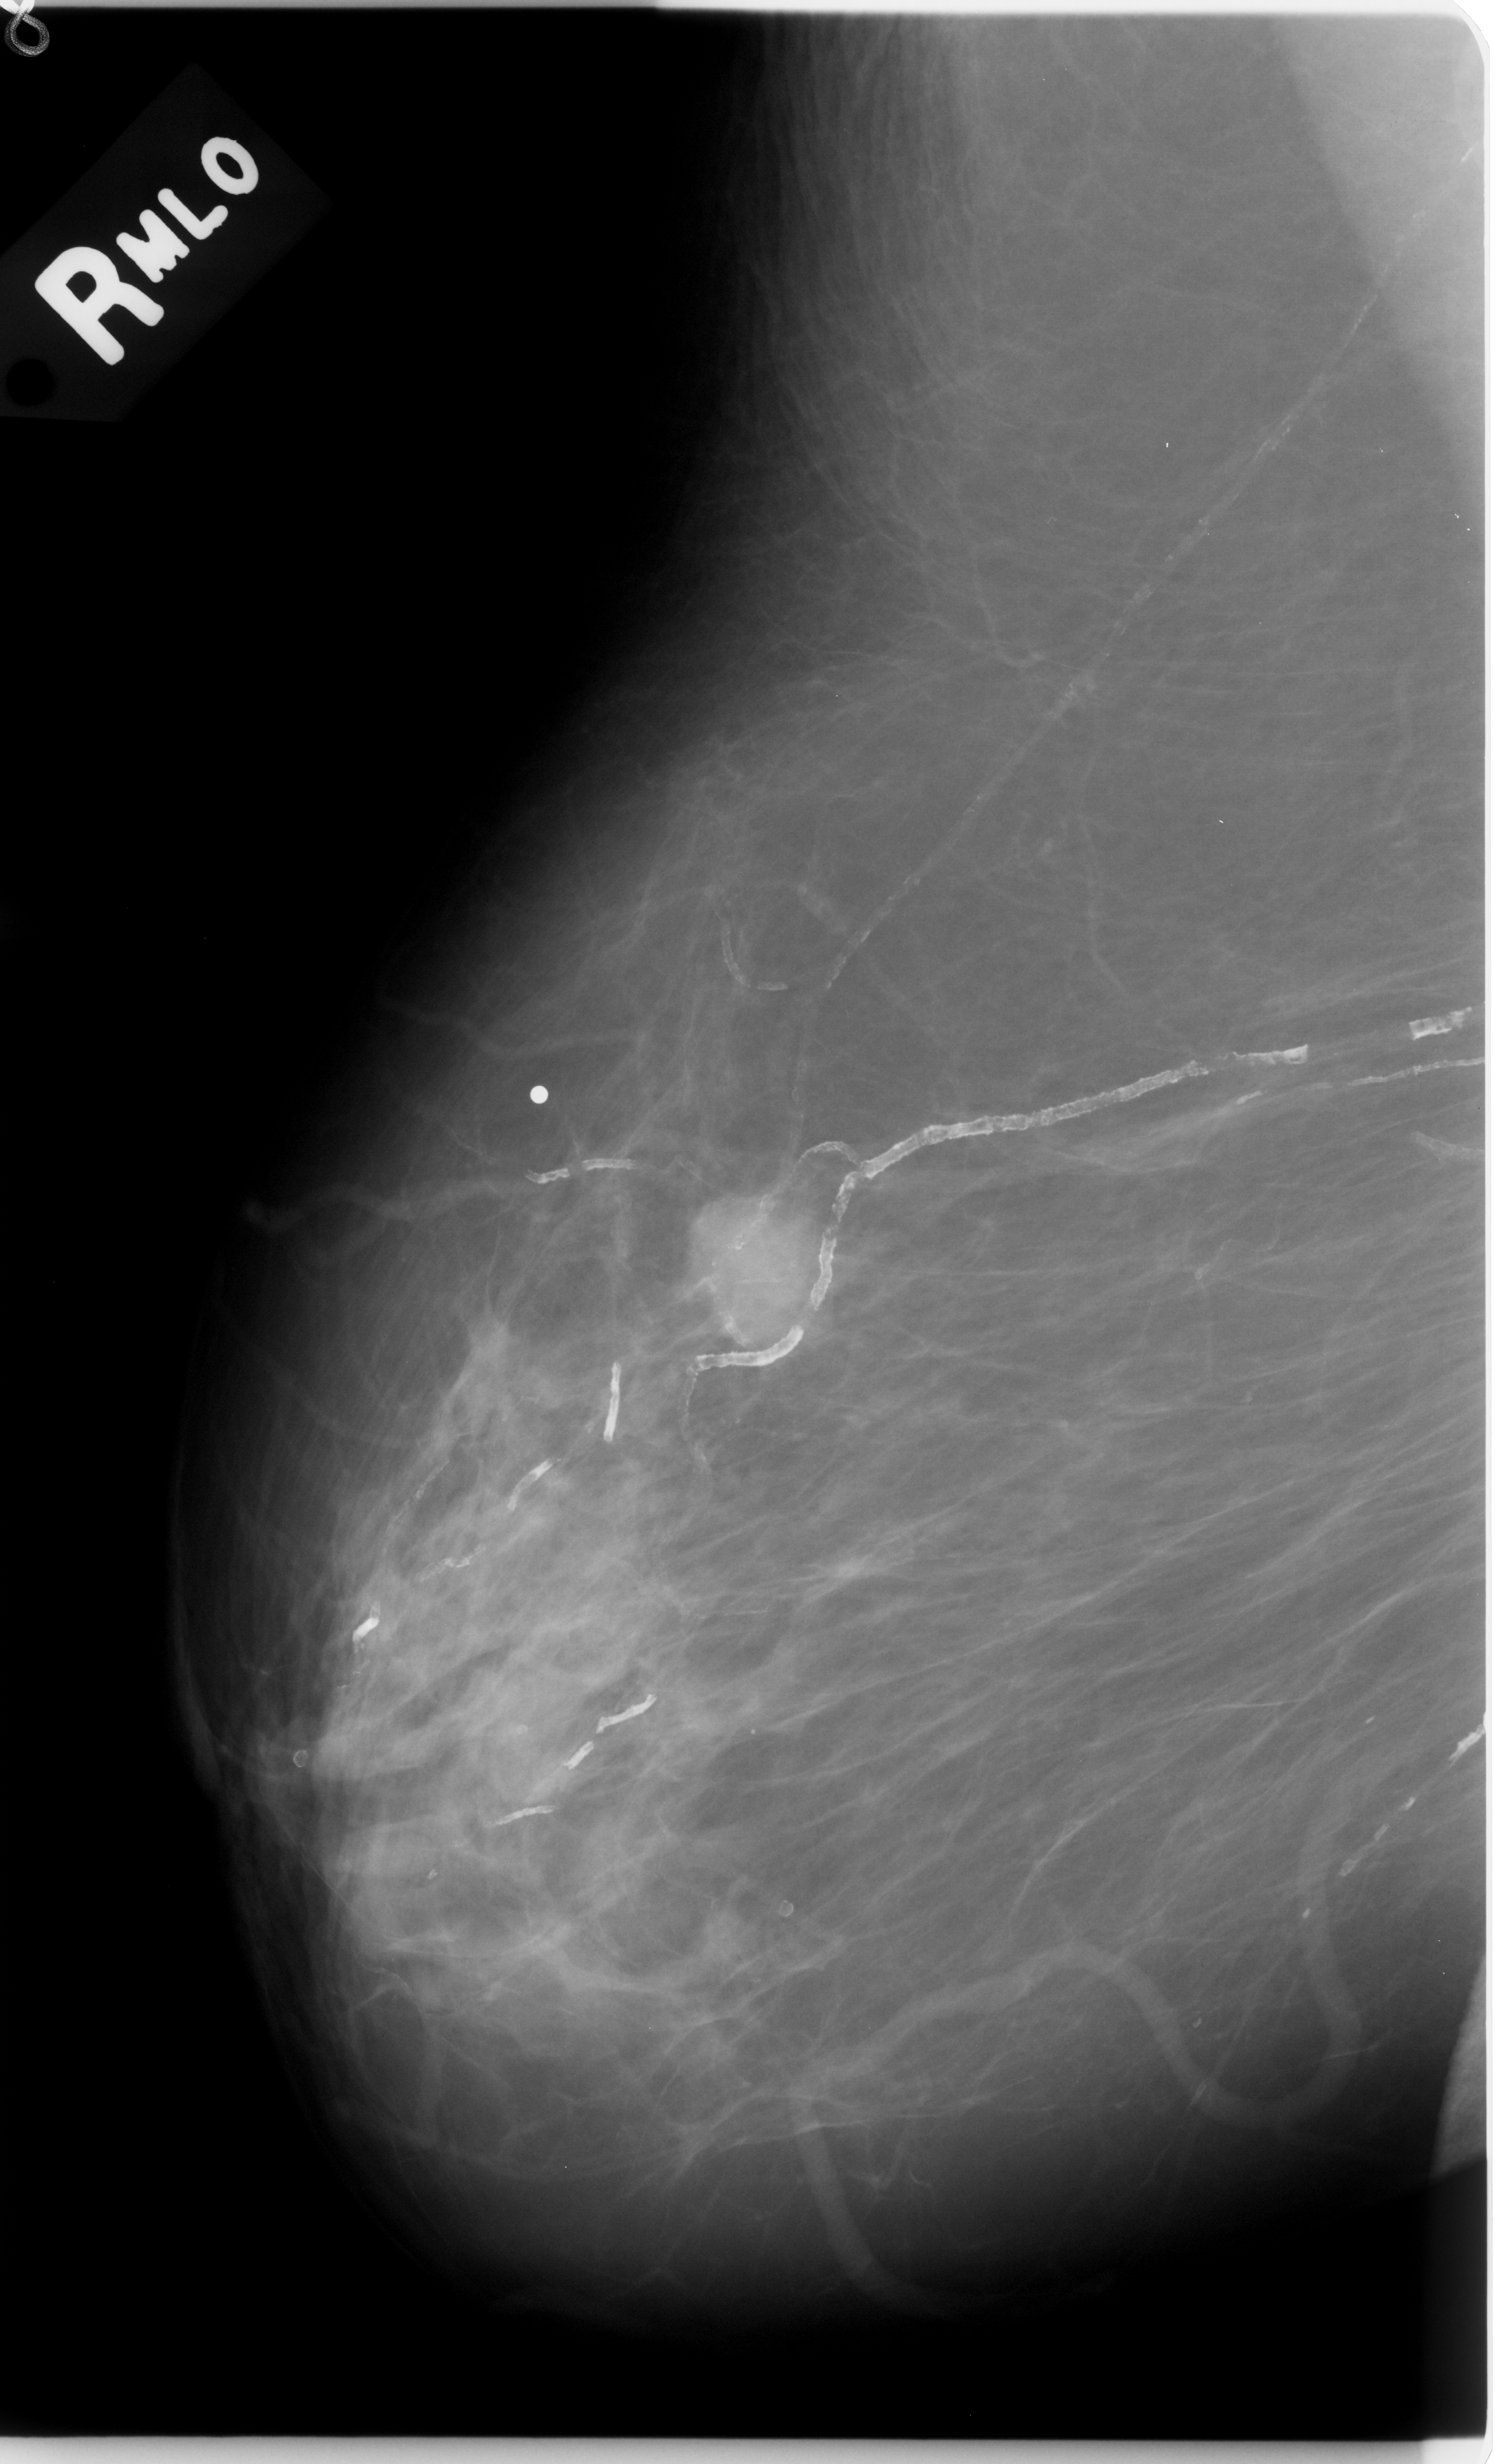
Digitized screen-film mammogram; right breast; mediolateral oblique (MLO) view; BI-RADS breast density category 1 (scale 1–4).
Finding: mass, shape irregular, margins microlobulated; BI-RADS assessment category 5; pathology result (as recorded, not read from the image): malignant.